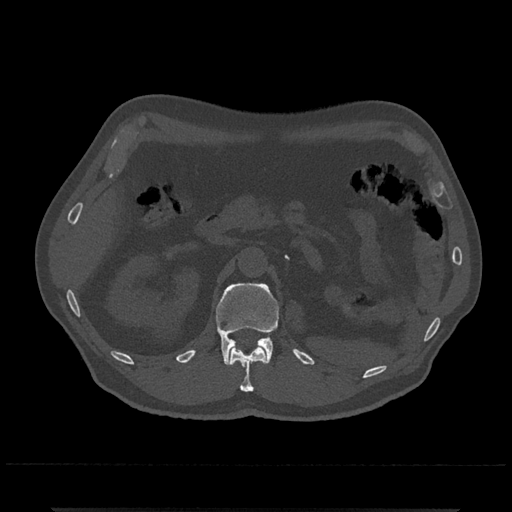
CT including the spine, one axial slice. Position 387 of 797 along the scan axis. Reconstruction kernel Br40s/3. 120 kVp. Bone window (W 1800 / L 400 HU). 512 × 512 image matrix. Male patient, age 67 years. From the clinical record (not read from this slice): primary cancer: prostate.
Annotated regions visible in this slice (semi-automatic segmentation, software-assisted and operator-edited):
- L1 vertebra: box from (x=216, y=283) to (x=279, y=365) px
- T12 vertebra: (x=230, y=346)–(x=267, y=392)